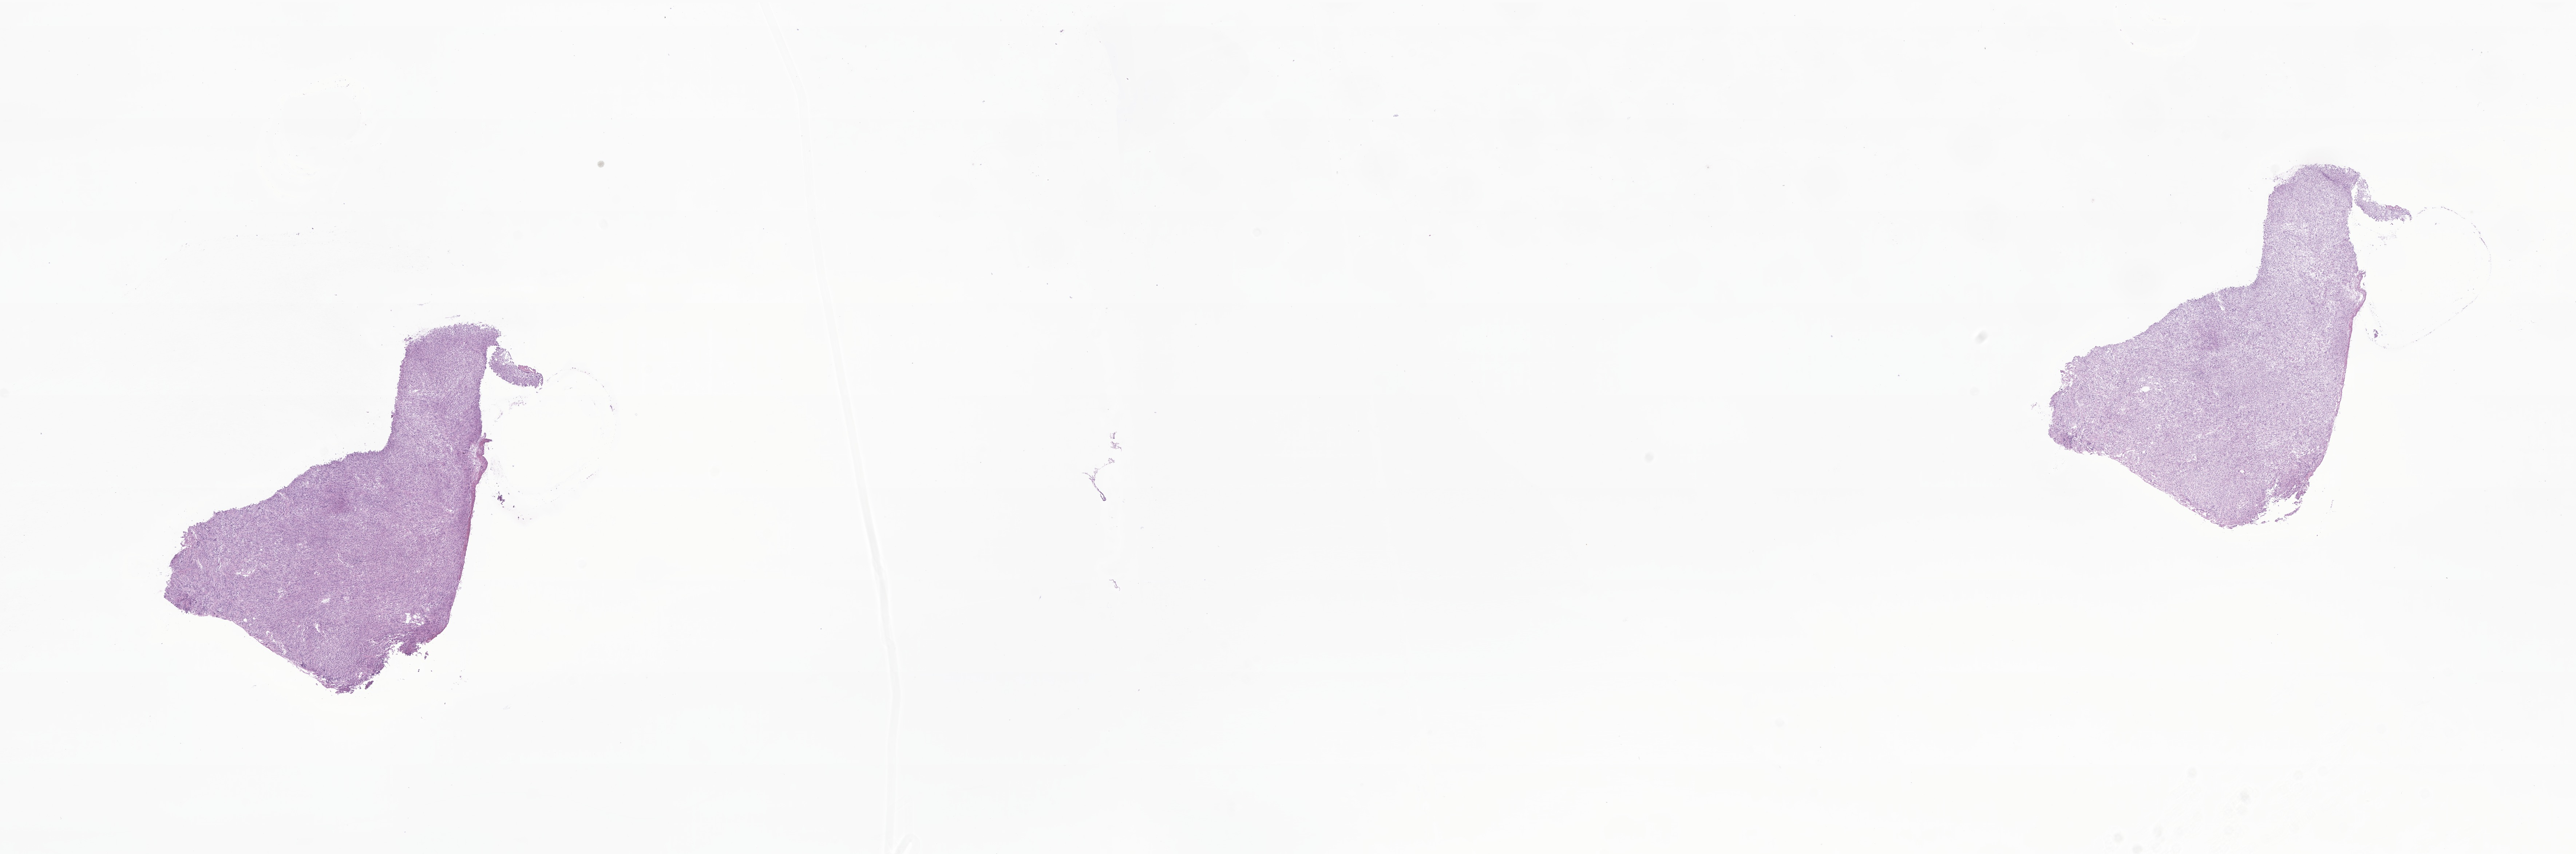
Digitized hematoxylin and eosin (H&E)-stained section of tumor tissue from the temporal lobe, low-resolution overview of the scanned area, about 29.8 x 9.9 mm. Frozen section. Patient female; age 47 months (3 years 11 months).
Diagnosis: Neoplasm, uncertain whether benign or malignant.